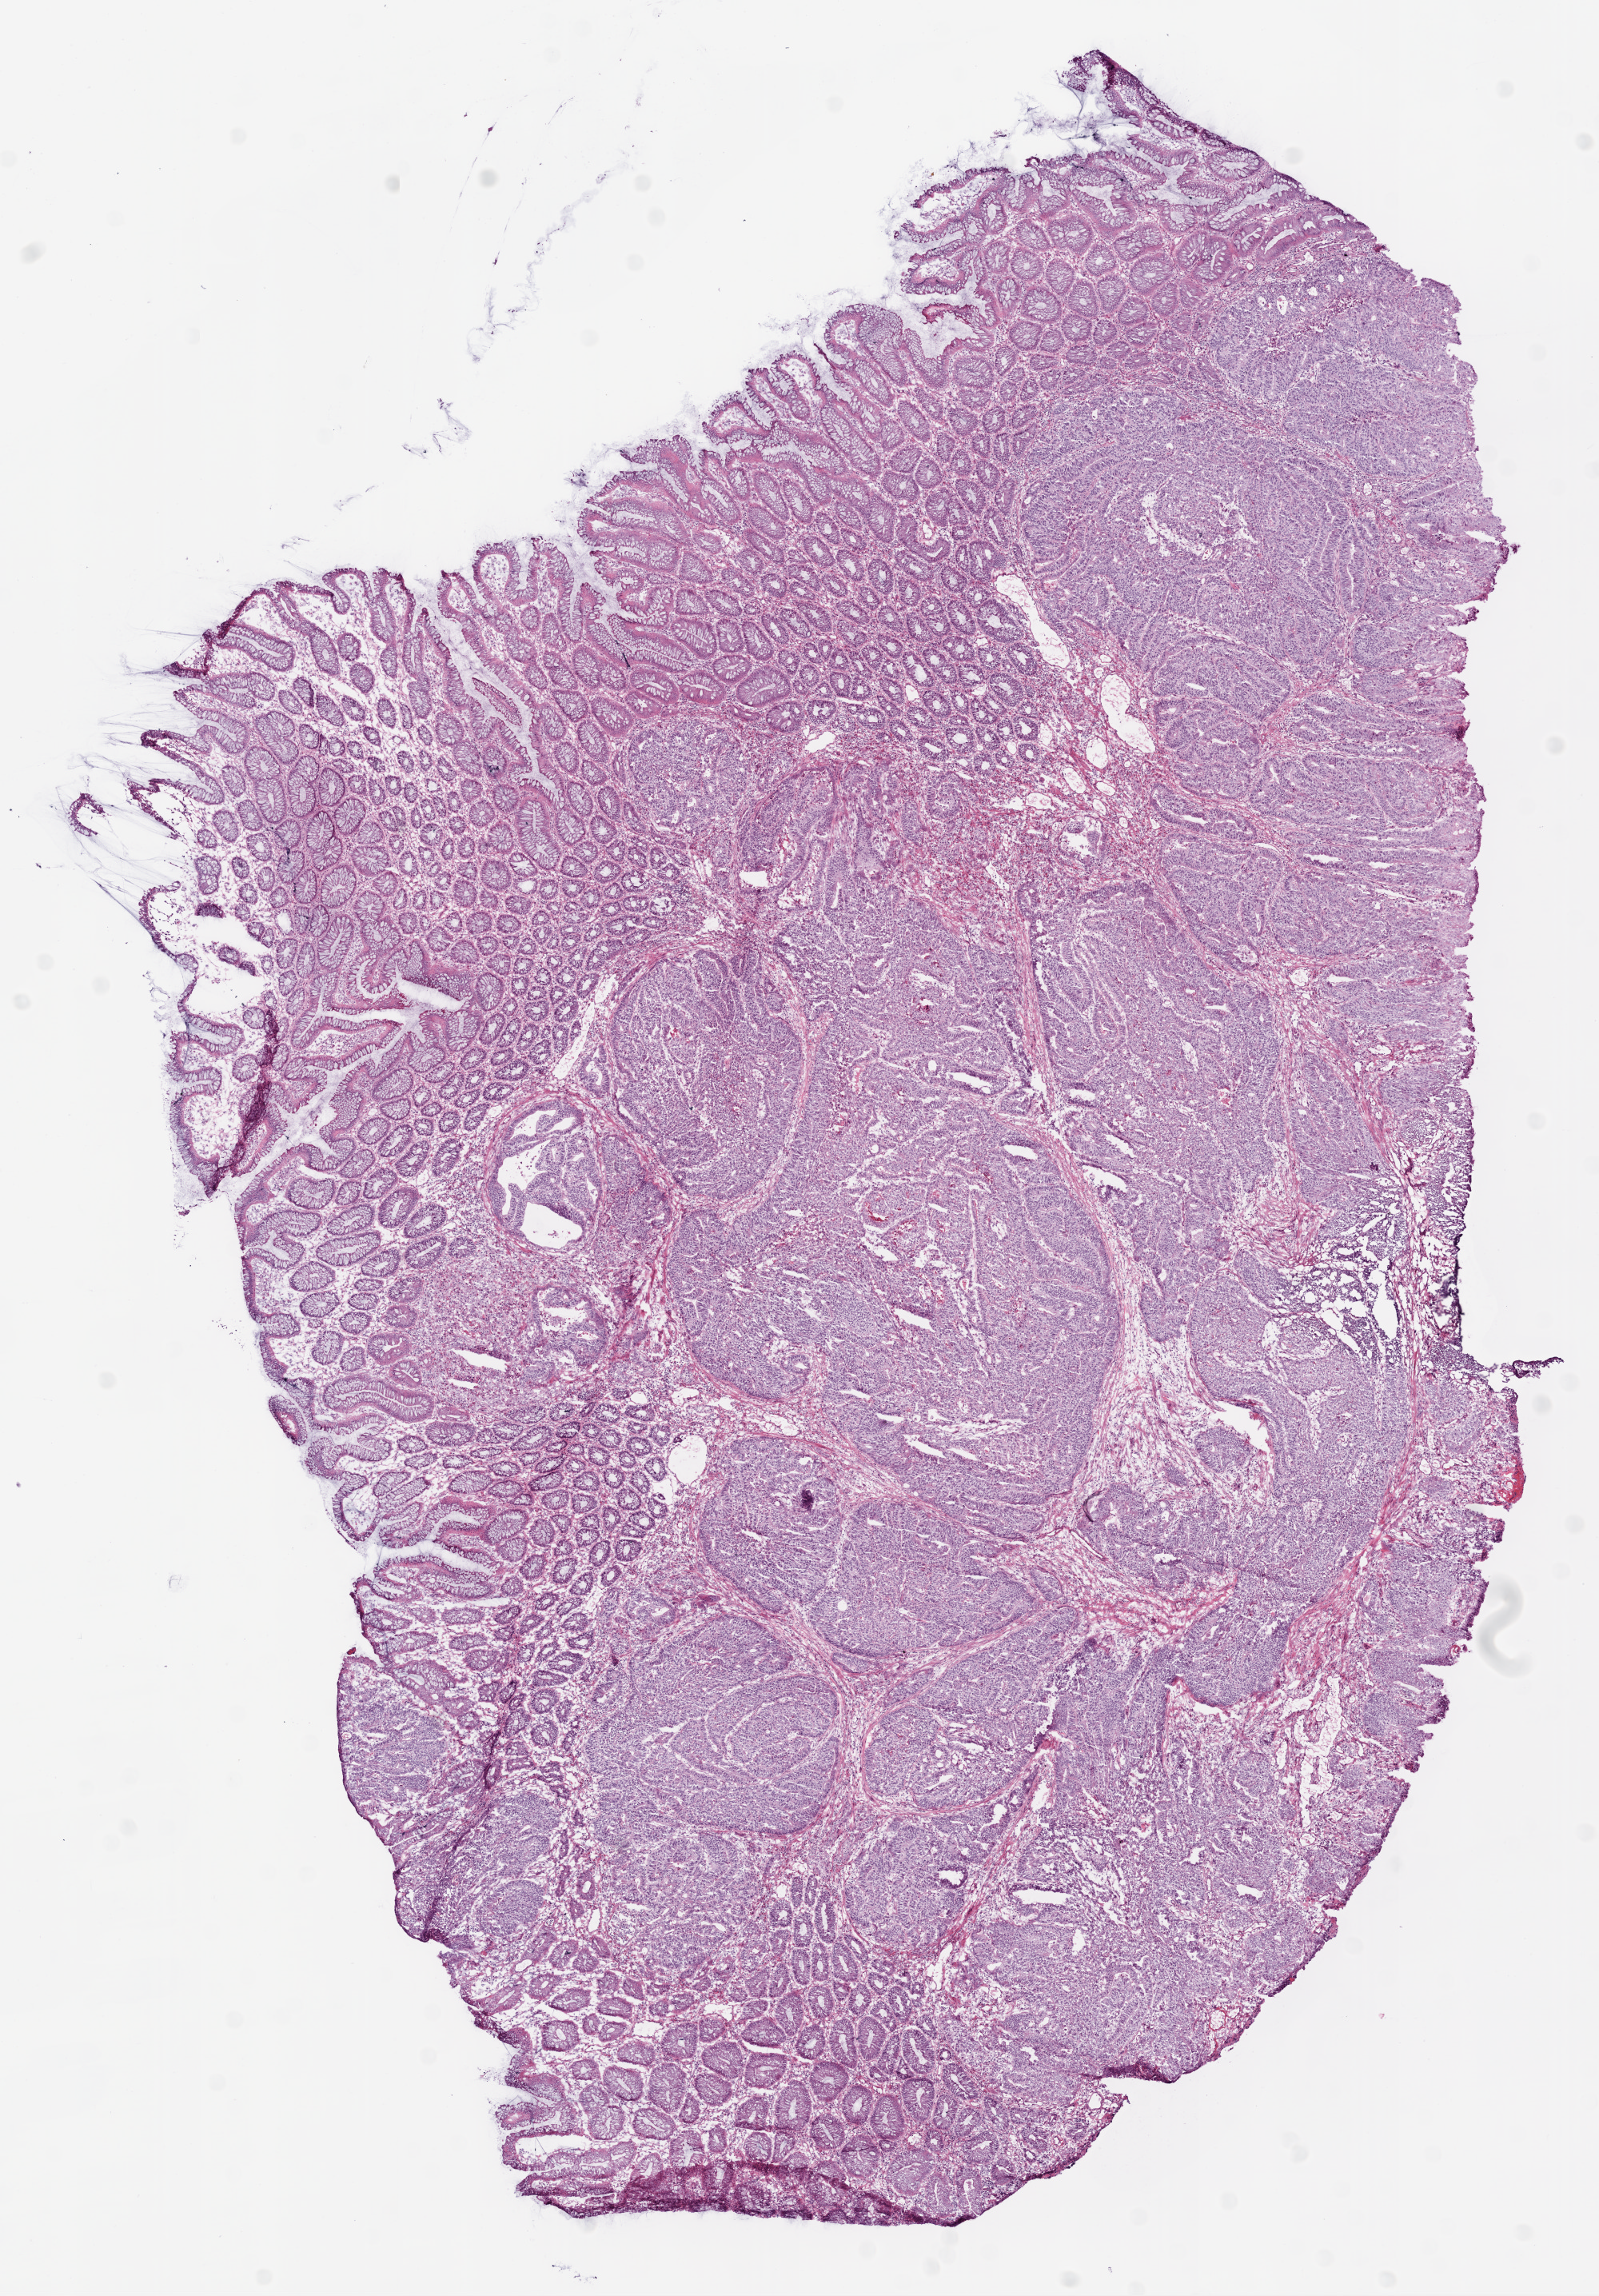
Whole-slide histology image, Hematoxylin and eosin (H&E) stained — low-resolution overview of the scanned area, about 8.0 x 11.5 mm (from a 20x scan); frozen section from the bottom of the tissue portion; colon, primary tumour sample. Female, age 78 years at initial diagnosis. Slide review estimates, as recorded: tumour cells 70%, tumour nuclei 80%.
Diagnosis: Adenocarcinoma, NOS.